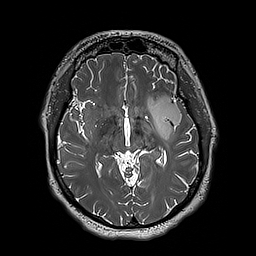
Brain MRI from a brain-tumour surgery series, one axial slice. Position 109 of 192 along the scan axis. 1 mm slice thickness. 256 × 256 image matrix. From the clinical record (not read from this slice): histopathology: Astrocytoma; WHO grade: 3; IDH mutation: yes; tumour location: Left Insular.
Structures marked on this image (expert manual segmentation):
- tumour: bounding box <148,95,182,141> (left, top, right, bottom; pixels)